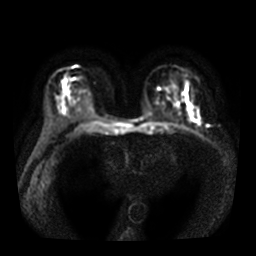
Breast MRI, one axial slice. Slice 19 of 36 in the series (ordered by position). Diffusion-weighted series; image 2 of 4 stored at this slice position (different b-values; order by instance number). 3 T. 5 mm slice thickness. 256 × 256 image matrix, field of view 320 × 320 mm. Female patient.
Outlined on this slice (outlined manually by an expert reader):
- tumour on diffusion-weighted imaging: bounding box <186,89,200,125> (left, top, right, bottom; pixels)